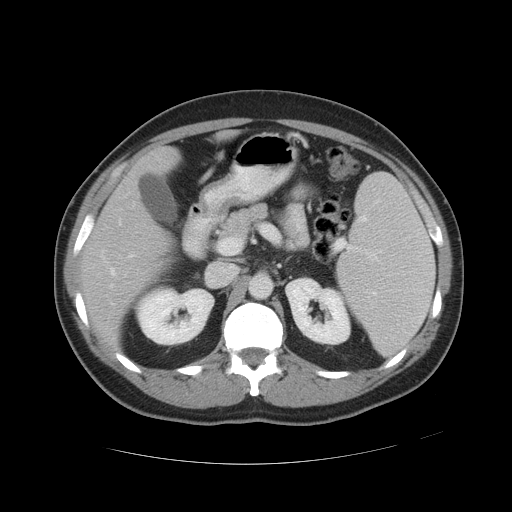
Contrast-enhanced abdominal CT, one axial slice; position 27 of 49 along the scan axis; 120 kVp; intravenous contrast given; soft-tissue window (W 400 / L 40 HU); 5 mm slice thickness; 512 × 512 image matrix, field of view 422 × 422 mm. Male patient, age 42 years. Case-level facts recorded for this patient, not image findings: diagnosis: colorectal cancer liver metastases, imaged before liver resection; multiple liver metastases: yes; largest metastasis: 2.8 cm; disease in both lobes: yes.
Outlined on this slice (manually delineated by an expert):
- hepatic veins: bounding box (x1, y1, x2, y2) in pixels: (110, 196, 135, 287)
- liver: (84, 150, 174, 344)
- planned liver remnant (the part of the liver to remain after resection): (84, 152, 172, 344)
- portal vein (with intrahepatic branches): (129, 254, 135, 257)